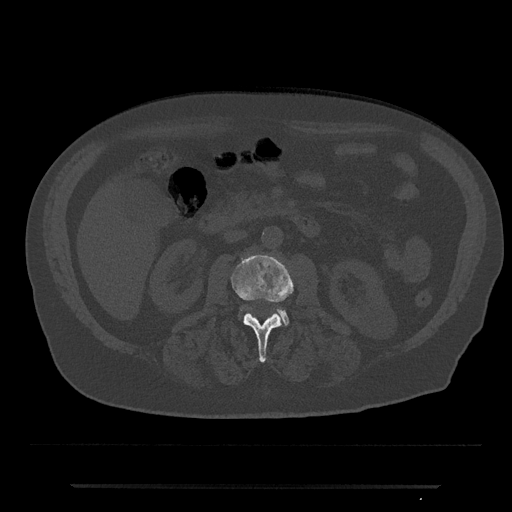
CT including the spine, one axial slice. Slice 453 of 797 in the series (ordered by position). Reconstruction kernel Br40s/3. Bone window (W 1800 / L 400 HU). 512 × 512 image matrix. Male patient, age 80 years. Case-level facts recorded for this patient, not image findings: primary cancer: prostate; vertebrae with lytic lesions (as recorded): L1, T11.
Outlined on this slice (semi-automatically segmented with operator editing):
- L2 vertebra: bounding box [x1, y1, x2, y2] px = [231, 255, 293, 363]
- L3 vertebra: [239, 308, 290, 326]